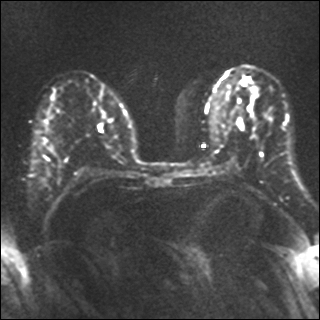
Breast MRI, one axial slice. Slice 17 of 40 in the series (ordered by position). Diffusion-weighted series; image 2 of 4 stored at this slice position (different b-values; order by instance number). 1.5 T. 320 × 320 image matrix, field of view 320 × 320 mm. Female patient.
Annotated regions visible in this slice (outlined manually by an expert reader):
- tumour on diffusion-weighted imaging: bounding box [x1, y1, x2, y2] px = [237, 122, 244, 130]